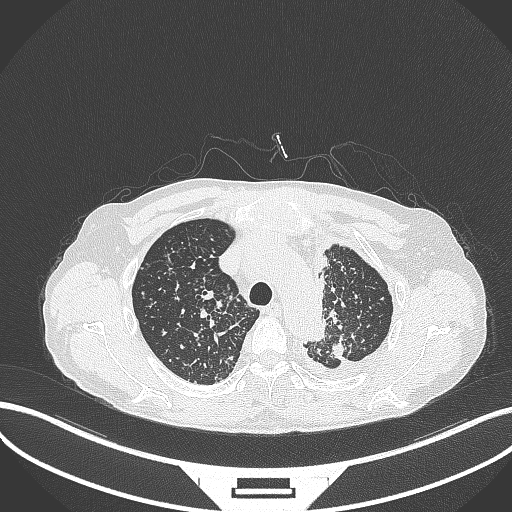
Chest CT, one axial slice; position 275 of 325 along the scan axis; reconstruction kernel B70f; 120 kVp; lung window (W 1500 / L -600 HU); 1 mm slice thickness; 512 × 512 image matrix, field of view 400 × 400 mm. Male patient, age 58 years. From the clinical record (not read from this slice): clinical TNM (as recorded): T1c N3 M1.
Structures marked on this image (rectangle marked by the reading radiologist):
- lung tumour (recorded histology: adenocarcinoma): bounding box (x1, y1, x2, y2) in pixels: (327, 335, 350, 361)